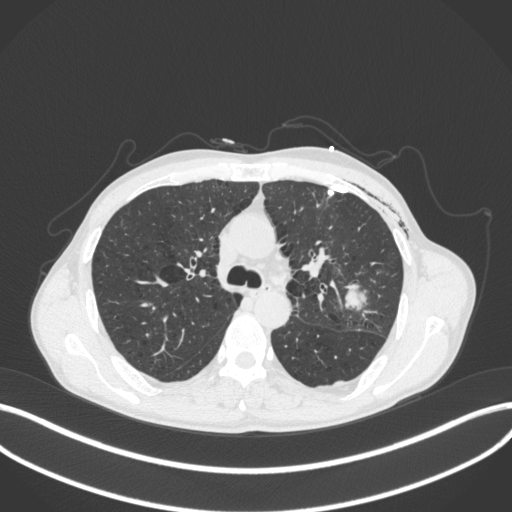
Chest CT, one axial slice; position 266 of 416 along the scan axis; reconstruction kernel B31f; 120 kVp; lung window (W 1500 / L -600 HU); 512 × 512 image matrix. Male patient, age 58 years. From the clinical record (not read from this slice): clinical TNM (as recorded): T3 N0 M0.
Annotated regions visible in this slice (rectangle marked by the reading radiologist):
- lung tumour (recorded histology: adenocarcinoma): box from (x=342, y=282) to (x=370, y=316) px